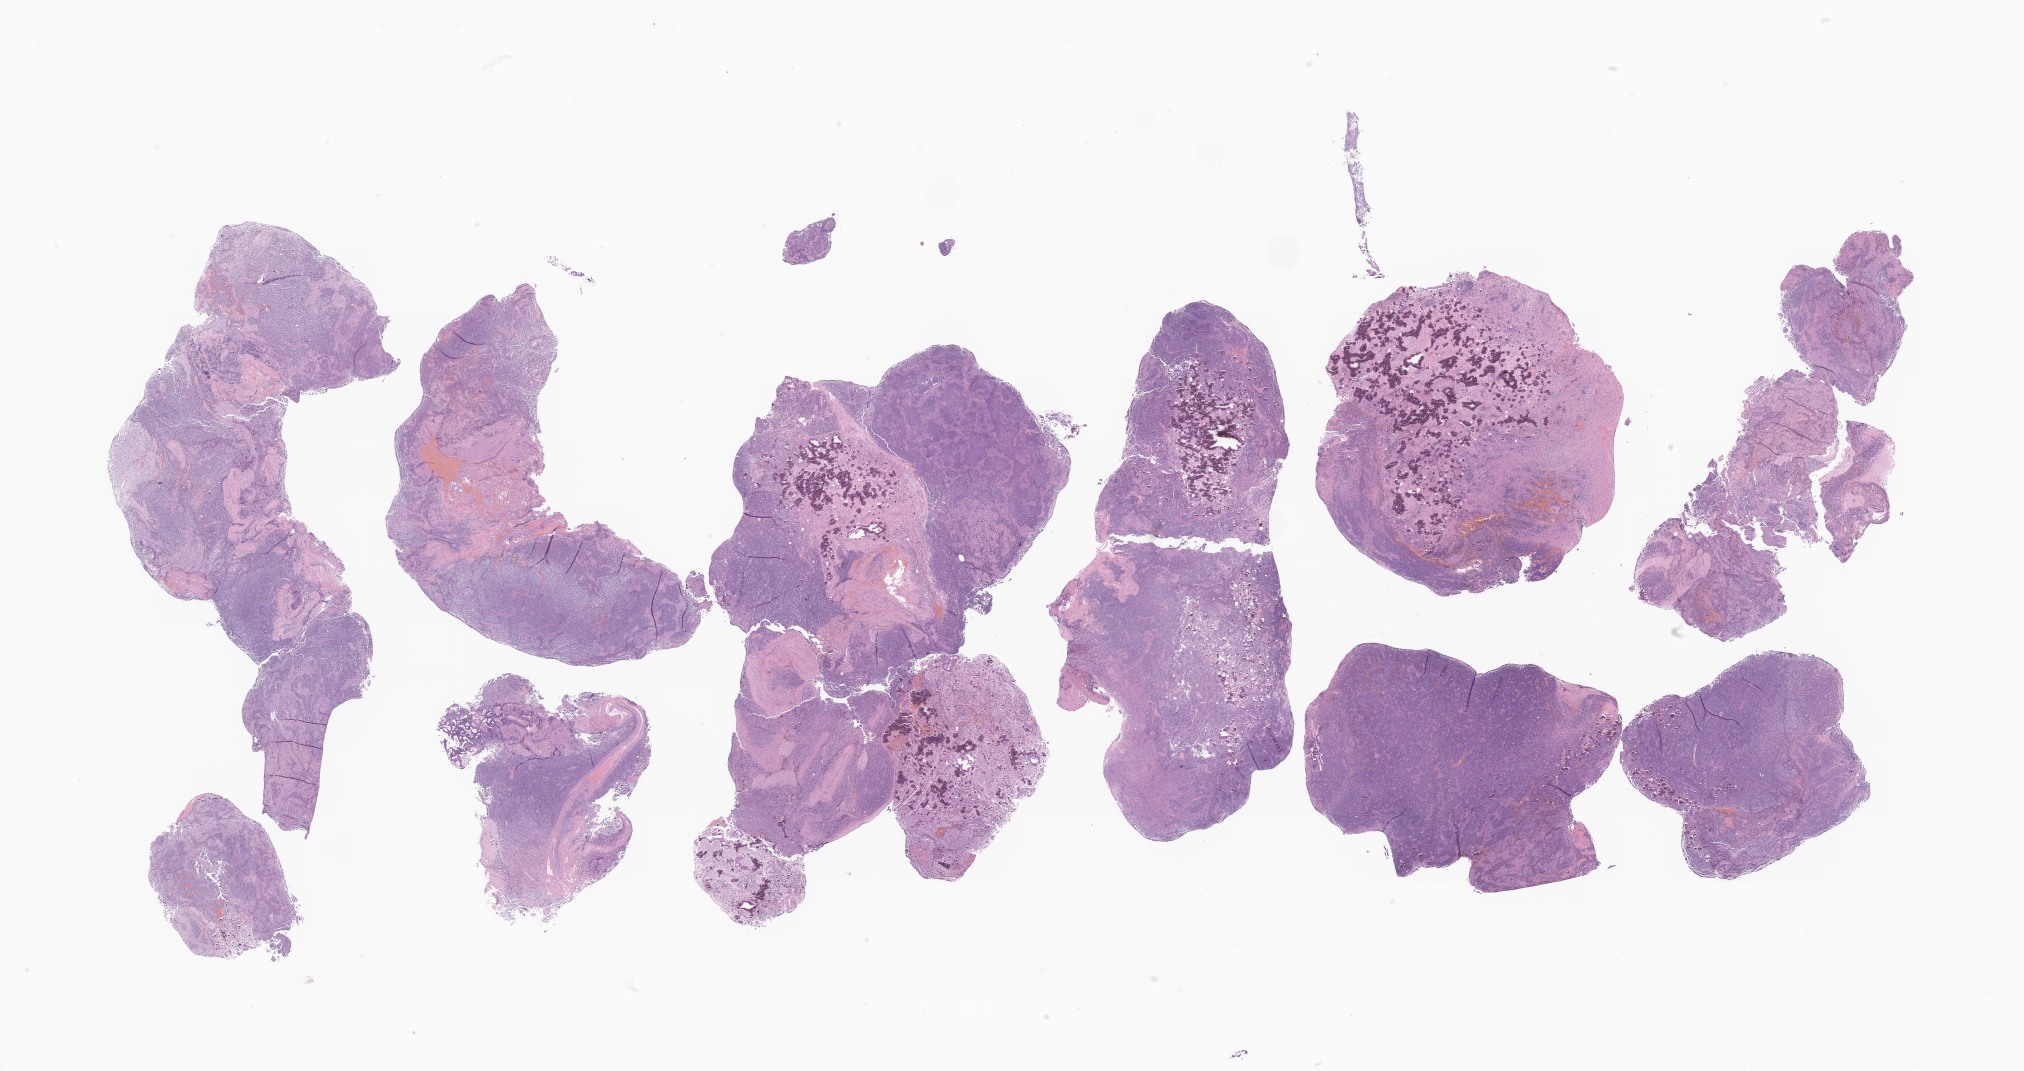
Whole-slide image, haematoxylin and eosin stain of tumor tissue from the brain — shown as a low-resolution overview of the whole scanned area (about 34.1 x 18.1 mm), FFPE section. Patient male; age 119 months (9 years 11 months).
Diagnosis (ICD-O-3 morphology term): Neoplasm, malignant.